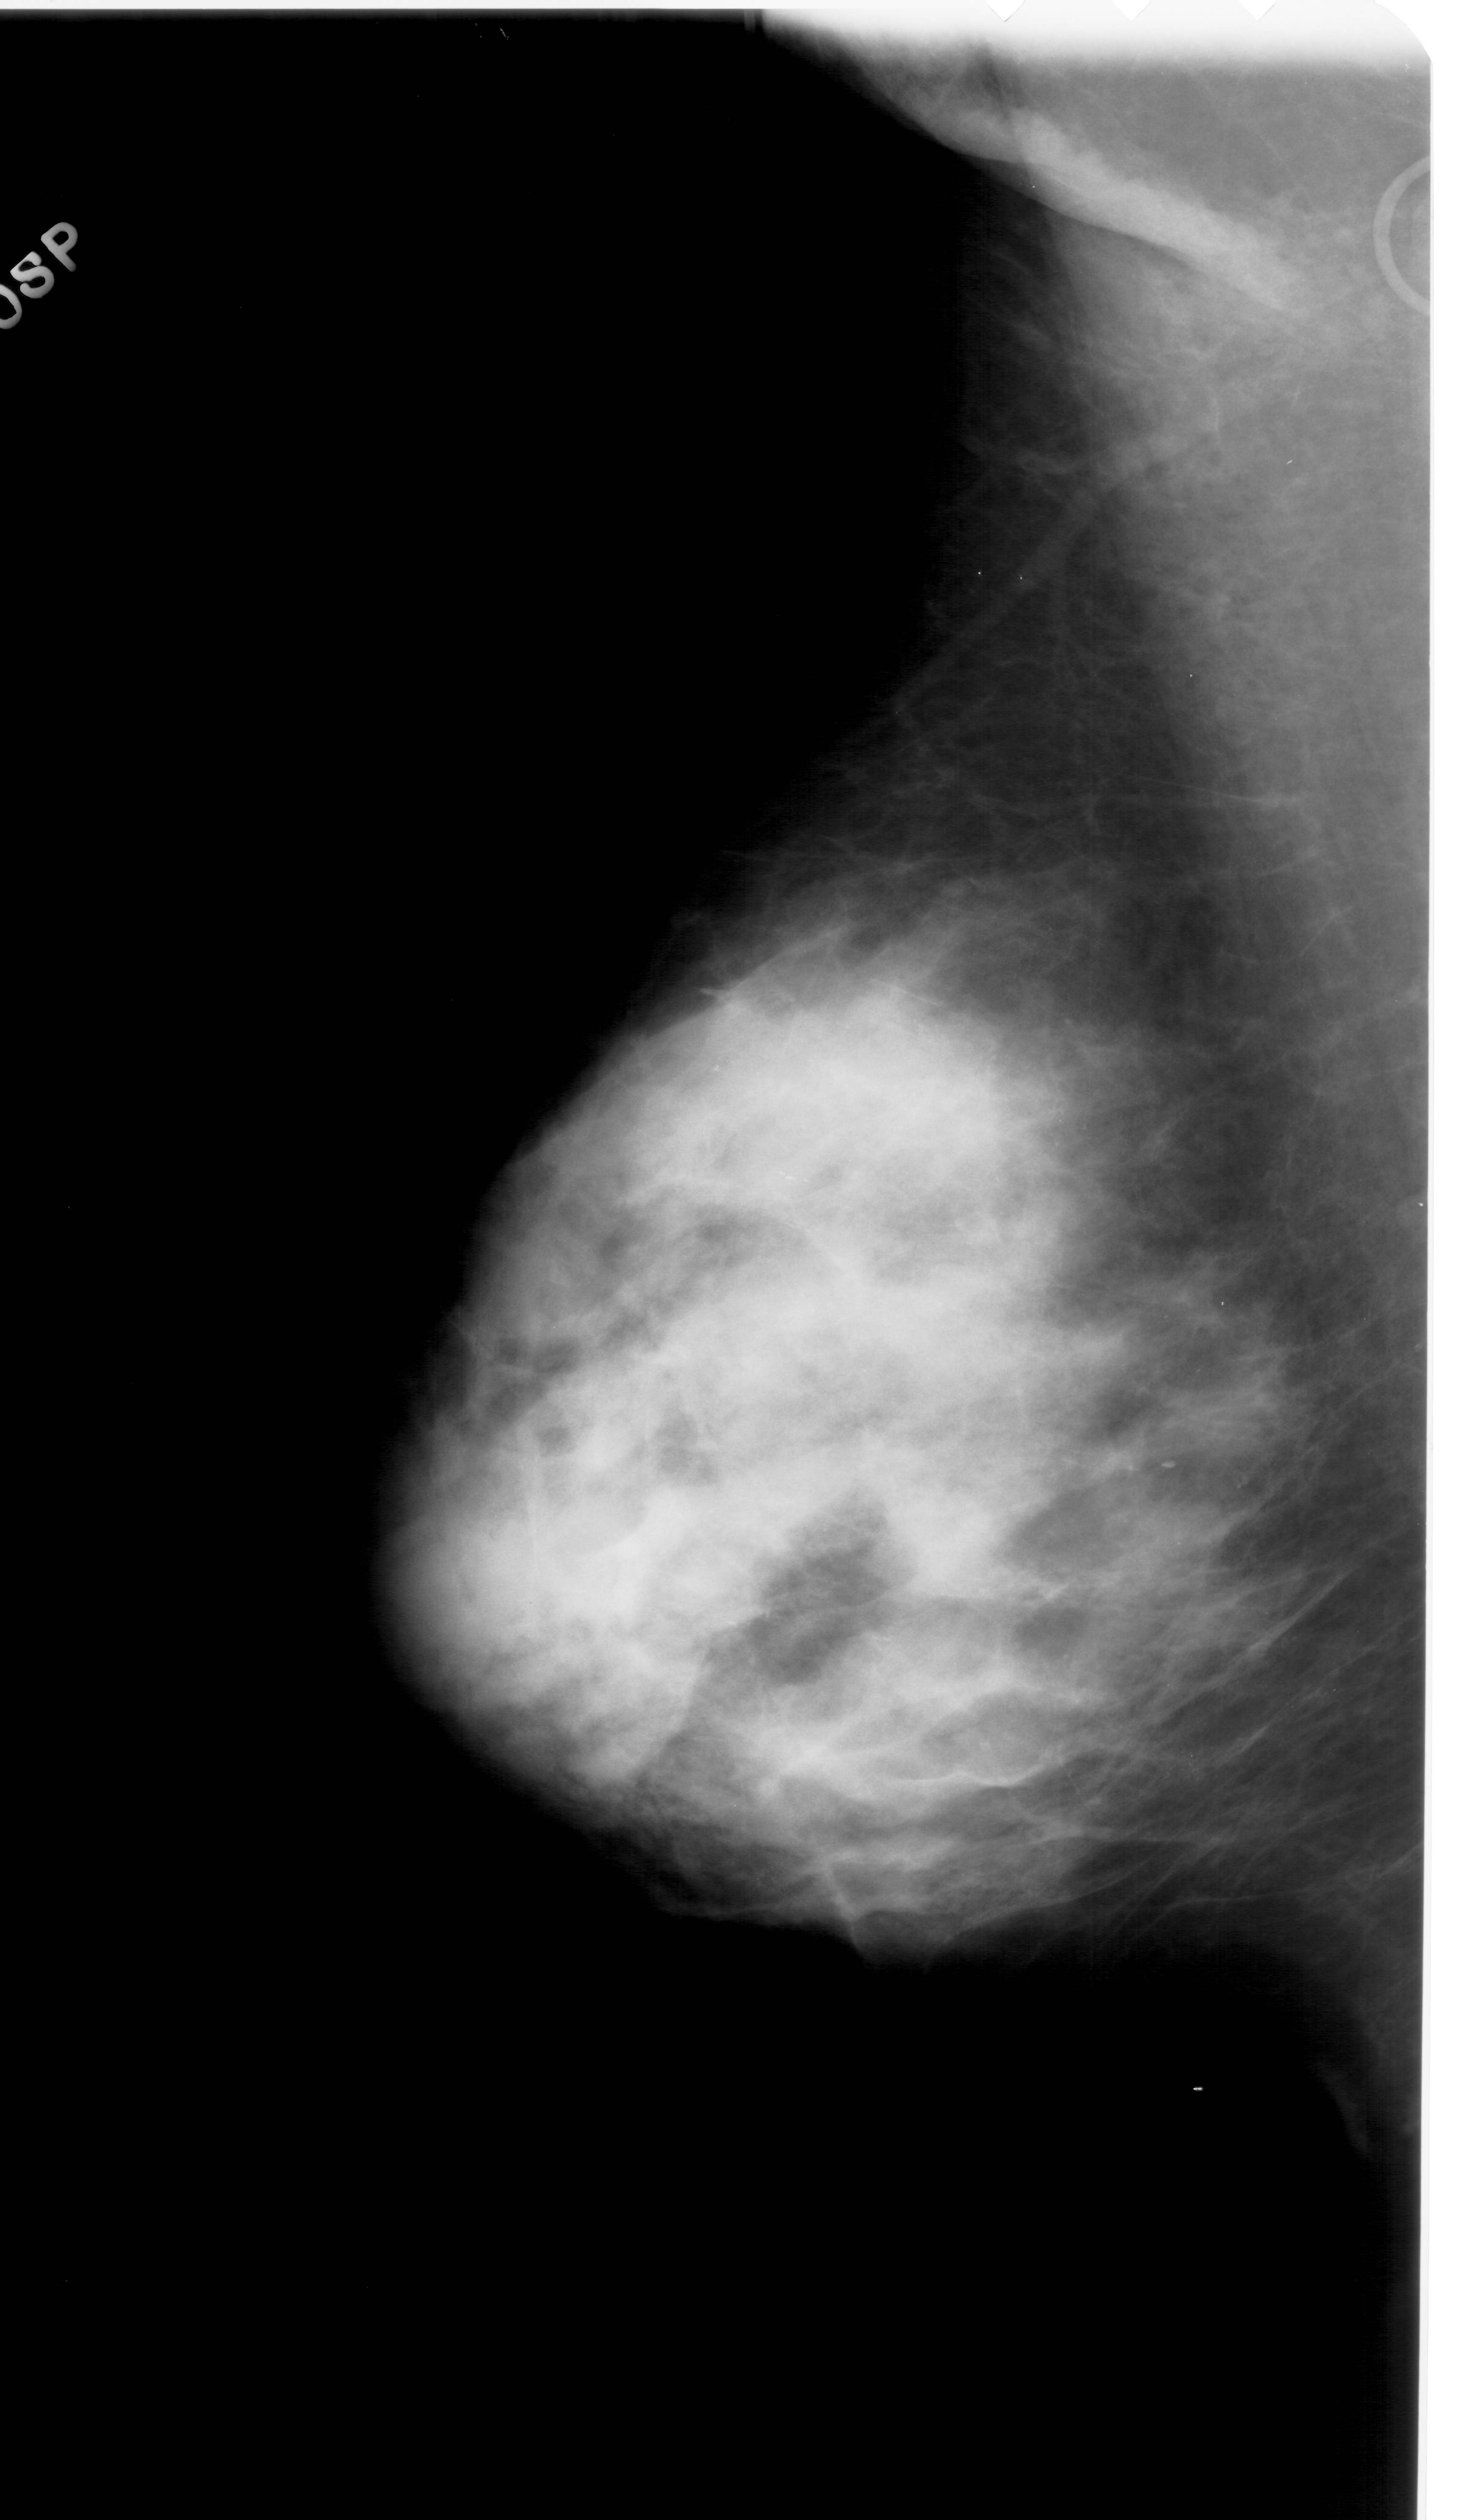
Mammogram (digitized film), left breast, MLO view, BI-RADS breast density category 4 (scale 1–4).
Abnormality record for this image: calcifications, morphology pleomorphic, distribution clustered; BI-RADS assessment category 4; pathology (as recorded): benign.